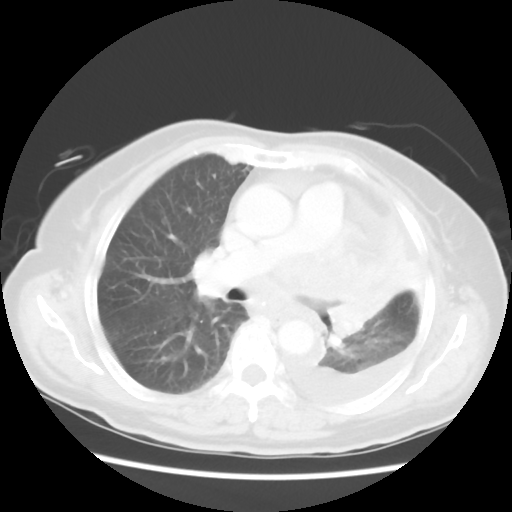
Chest CT, one axial slice; position 32 of 52 along the scan axis; reconstruction kernel STANDARD; 120 kVp; lung window (W 1500 / L -600 HU); 5 mm slice thickness; 512 × 512 image matrix, field of view 336 × 336 mm. Patient: female, 72 years. Case-level facts recorded for this patient, not image findings: clinical TNM (as recorded): T4 N3 M1b.
Structures marked on this image (rectangle marked by the reading radiologist):
- lung tumour (recorded histology: large cell carcinoma): bounding box [x1, y1, x2, y2] px = [304, 247, 391, 351]